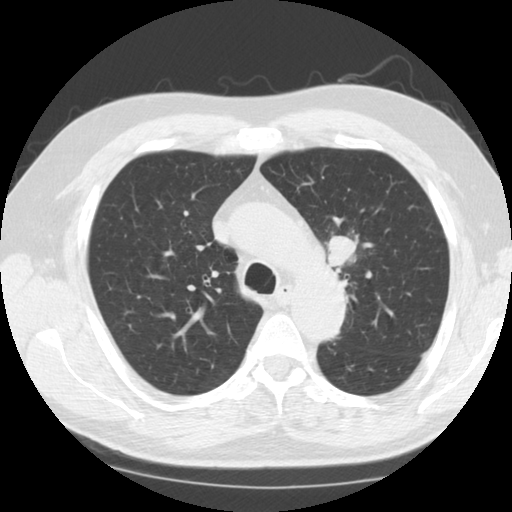
Low-dose screening chest CT, one axial slice. Reconstruction kernel STANDARD. 120 kVp. Lung window (W 1500 / L -600 HU). 2.5 mm slice thickness. 512 × 512 image matrix, field of view 340 × 340 mm.
Outlined on this slice (manually delineated by an expert):
- lesion 1 (tumor, upper lobe of left lung): bounding box <327,235,357,266> (left, top, right, bottom; pixels)